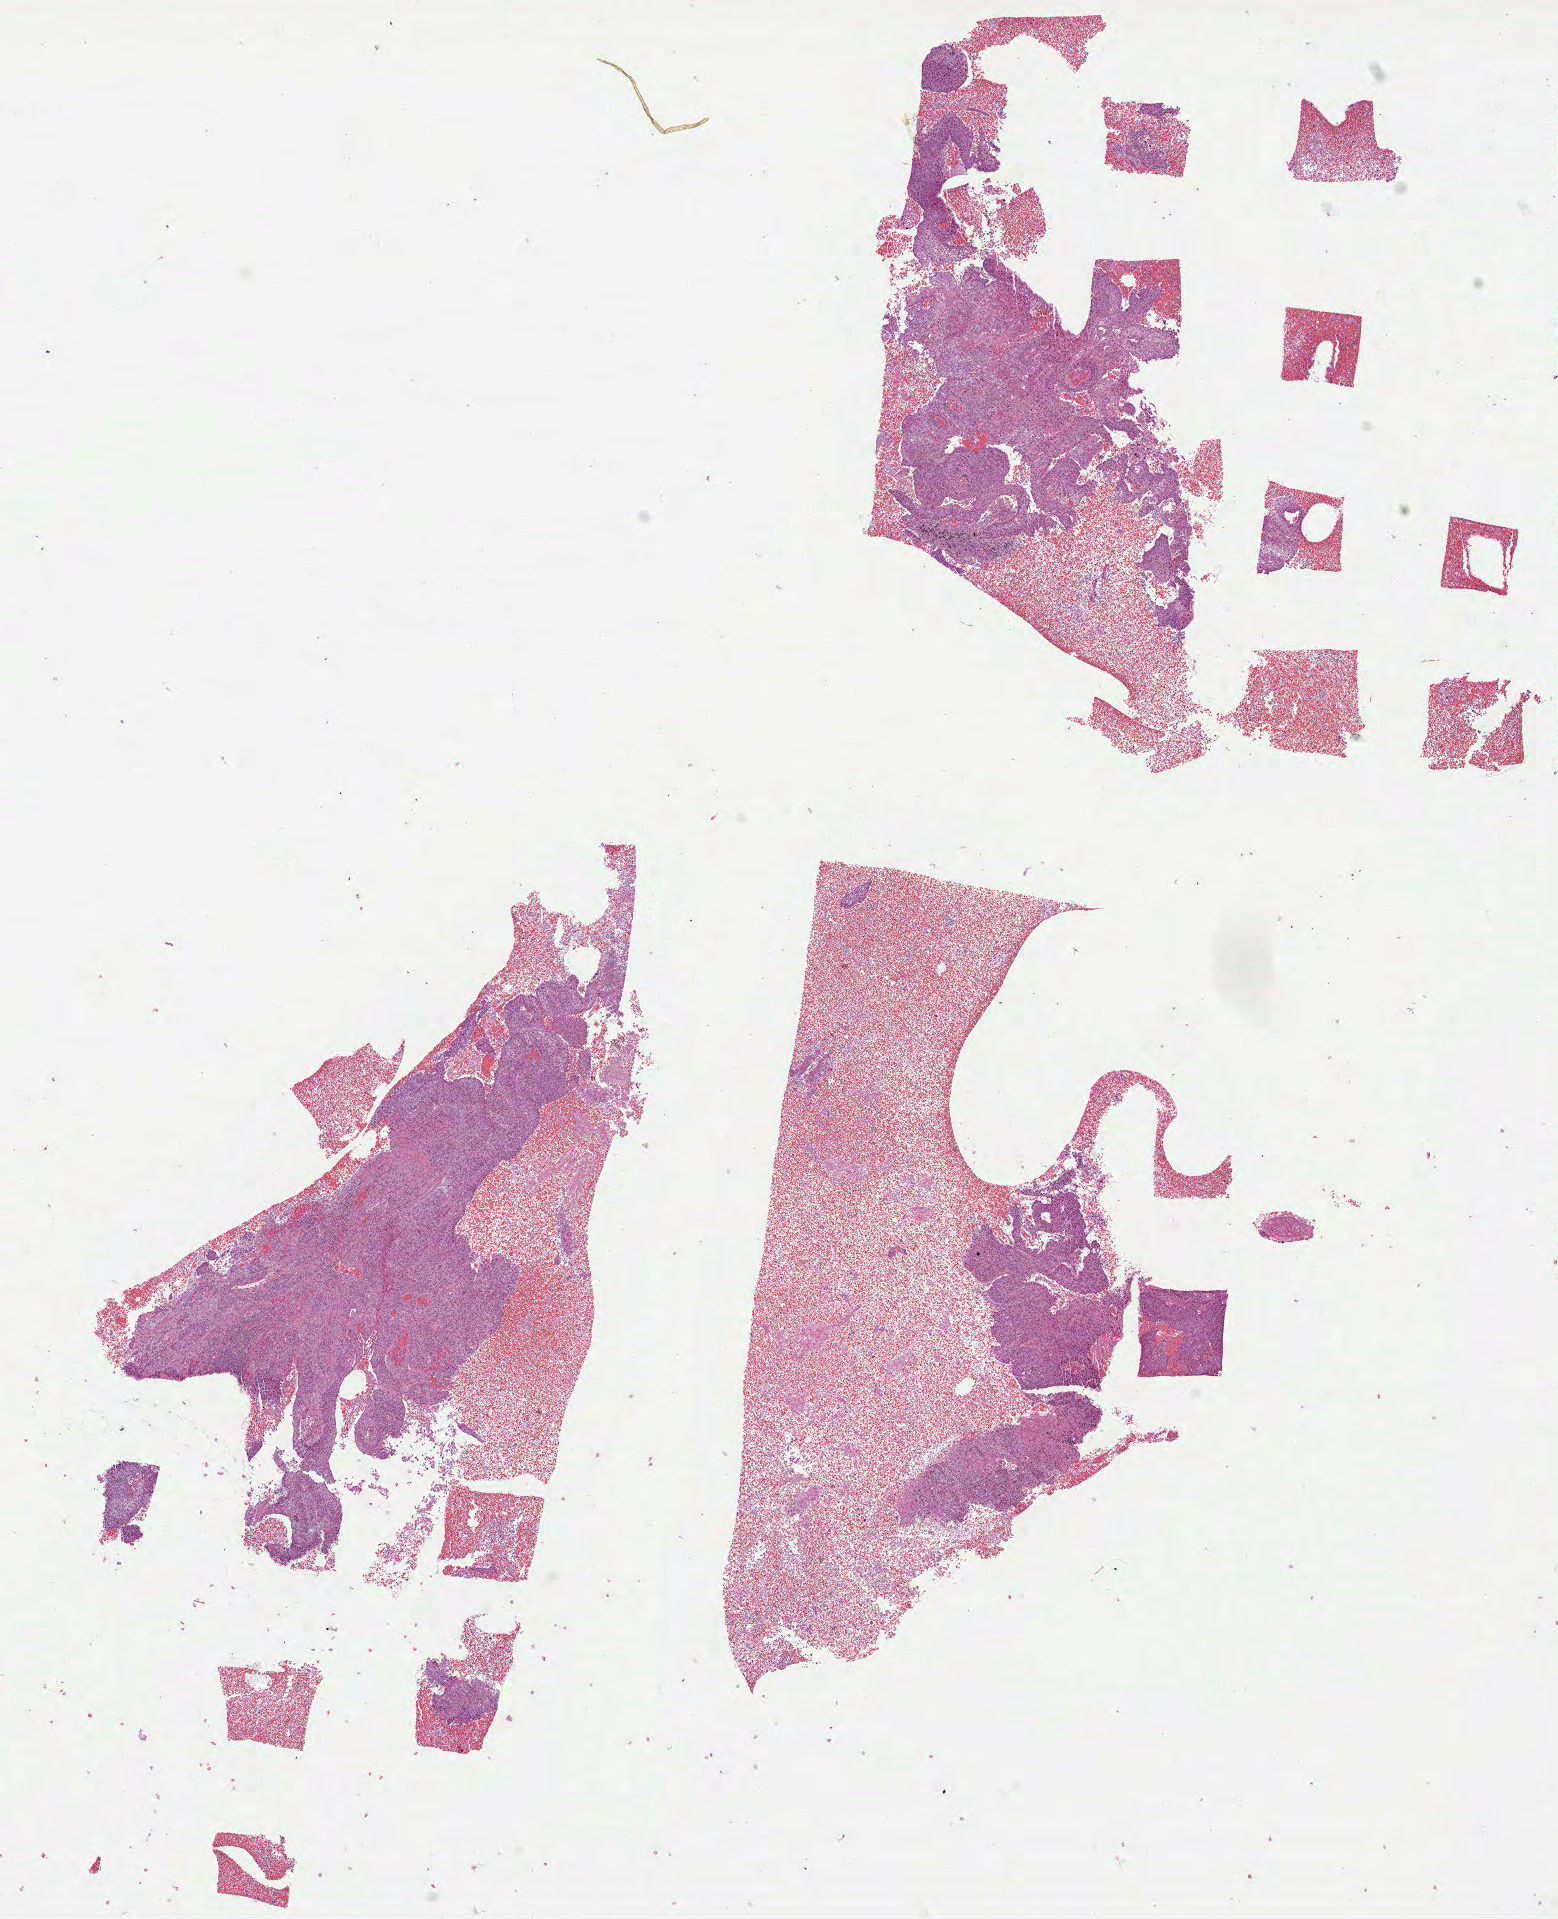
H&E whole-slide image, a low-resolution overview of the entire scanned area, about 12.6 x 15.5 mm (from a 40x scan); formalin-fixed paraffin-embedded (FFPE) diagnostic section; primary tumour sample from the lung. Male patient; age at initial diagnosis 74 years.
Pathologic diagnosis: Squamous cell carcinoma, NOS (upper lobe, lung).